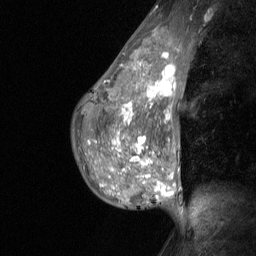
Breast MRI (dynamic contrast-enhanced), one sagittal slice; slice 41 of 64 in the series (ordered by position); dynamic contrast-enhanced study with each time point stored as its own series, time point 2 of 3 at this slice position (early post-contrast, ordered by acquisition time); 1.5 T; TE 4.8 ms, TR 27 ms; 2 mm slice thickness; 256 × 256 image matrix. Patient: female, 36 years. From the clinical record (not read from this slice): setting: breast cancer imaged before/during neoadjuvant chemotherapy; receptor status: HR-positive, HER2-negative.
Annotated regions visible in this slice (semi-automatic segmentation, software-assisted and operator-edited):
- analysis volume of interest (the breast-tissue region the enhancement analysis was run in; not a lesion): box from (x=73, y=45) to (x=185, y=210) px
- tumour enhancement mask (voxels above the 90 % enhancement threshold inside the analysis volume of interest): (x=89, y=53)–(x=176, y=198)